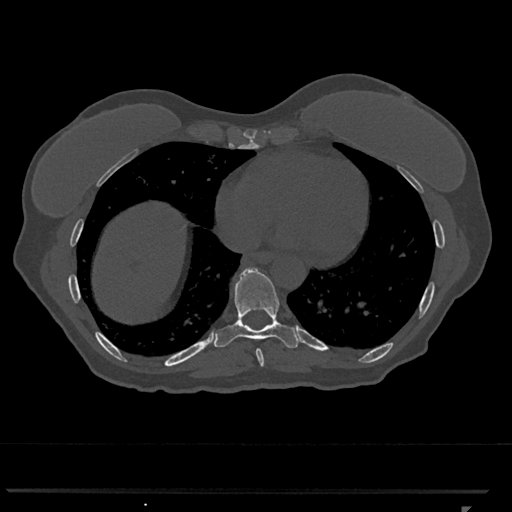
CT including the spine, one axial slice. Position 622 of 793 along the scan axis. Reconstruction kernel Br40s/3. 120 kVp. Bone window (W 1800 / L 400 HU). 0.5 mm slice thickness. 512 × 512 image matrix. Female patient, age 62 years. Case-level facts recorded for this patient, not image findings: primary cancer: renal.
Outlined on this slice (semi-automatic segmentation, software-assisted and operator-edited):
- T8 vertebra: bounding box [x1, y1, x2, y2] px = [256, 348, 265, 367]
- T9 vertebra: [214, 268, 299, 348]